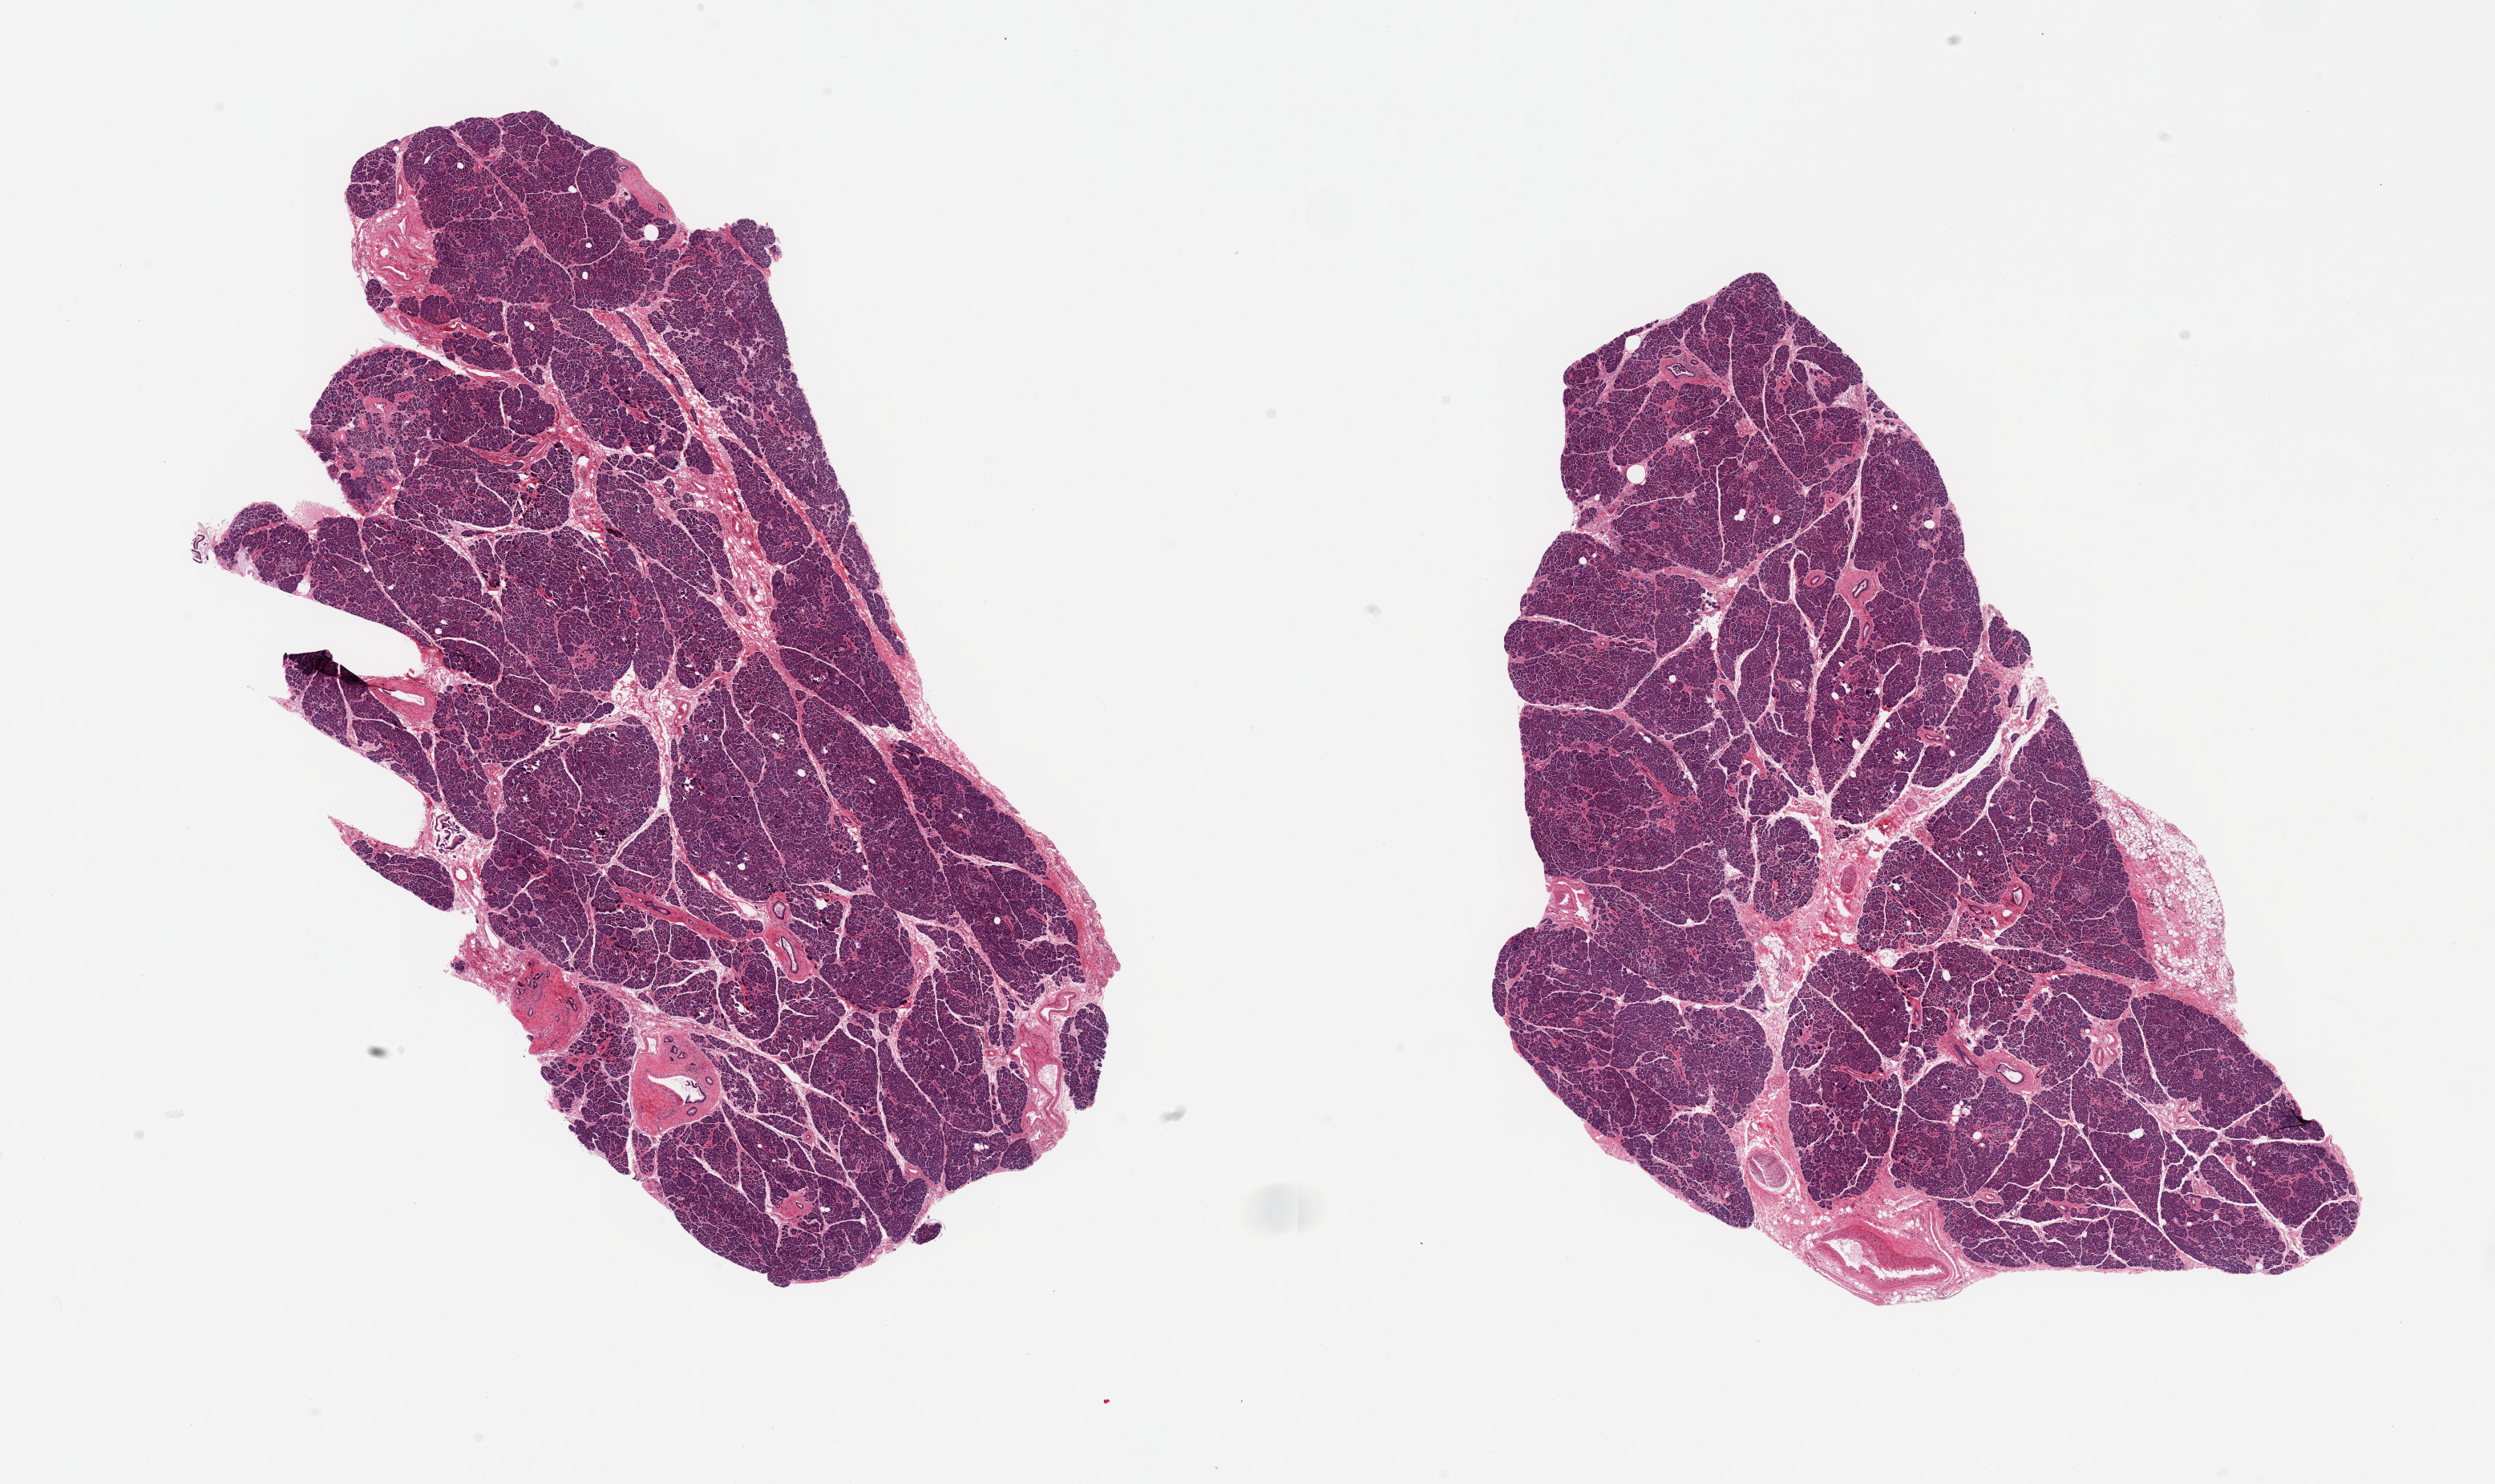
Whole-slide image, H&E stain, a low-resolution overview of the entire scanned area, about 24.6 x 14.6 mm (slide scanned at 20x). PAXgene-fixed paraffin-embedded (PFPE) section. Sampled site (target tissue): pancreas. Donor tissue sample. Male donor.
Review note (as recorded): 2 pieces, Islets infrequent but fairly well preserved; Few foci are approaching more moderate saponification.